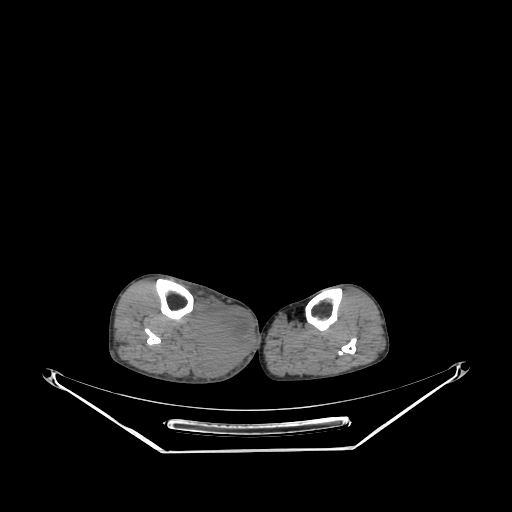
CT of an extremity soft-tissue mass (from a PET/CT study), one axial slice. Slice 135 of 267 in the series (ordered by position). Reconstruction kernel SOFT. 140 kVp. Soft-tissue window (W 400 / L 40 HU). 3.75 mm slice thickness. 512 × 512 image matrix, field of view 500 × 500 mm. Male patient. Case-level facts recorded for this patient, not image findings: histological type: pleiomorphic liposarcoma; grade: high; site of the primary tumour: right calf.
Annotated regions visible in this slice (expert contour drawn on MRI and transferred to this co-registered scan by the dataset authors):
- gross tumour volume including surrounding oedema: bounding box (x1, y1, x2, y2) in pixels: (194, 297, 254, 378)
- gross tumour volume (mass): (194, 304, 254, 364)